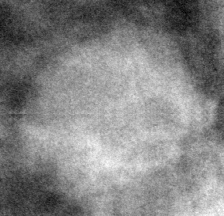
Region of interest cut from a scanned film mammogram (one marked finding), left breast, MLO view.
- Finding: mass, shape oval, margins circumscribed; BI-RADS assessment category 3; subtlety rating 5 on a 1 (subtle) to 5 (obvious) scale; pathology (as recorded): benign.